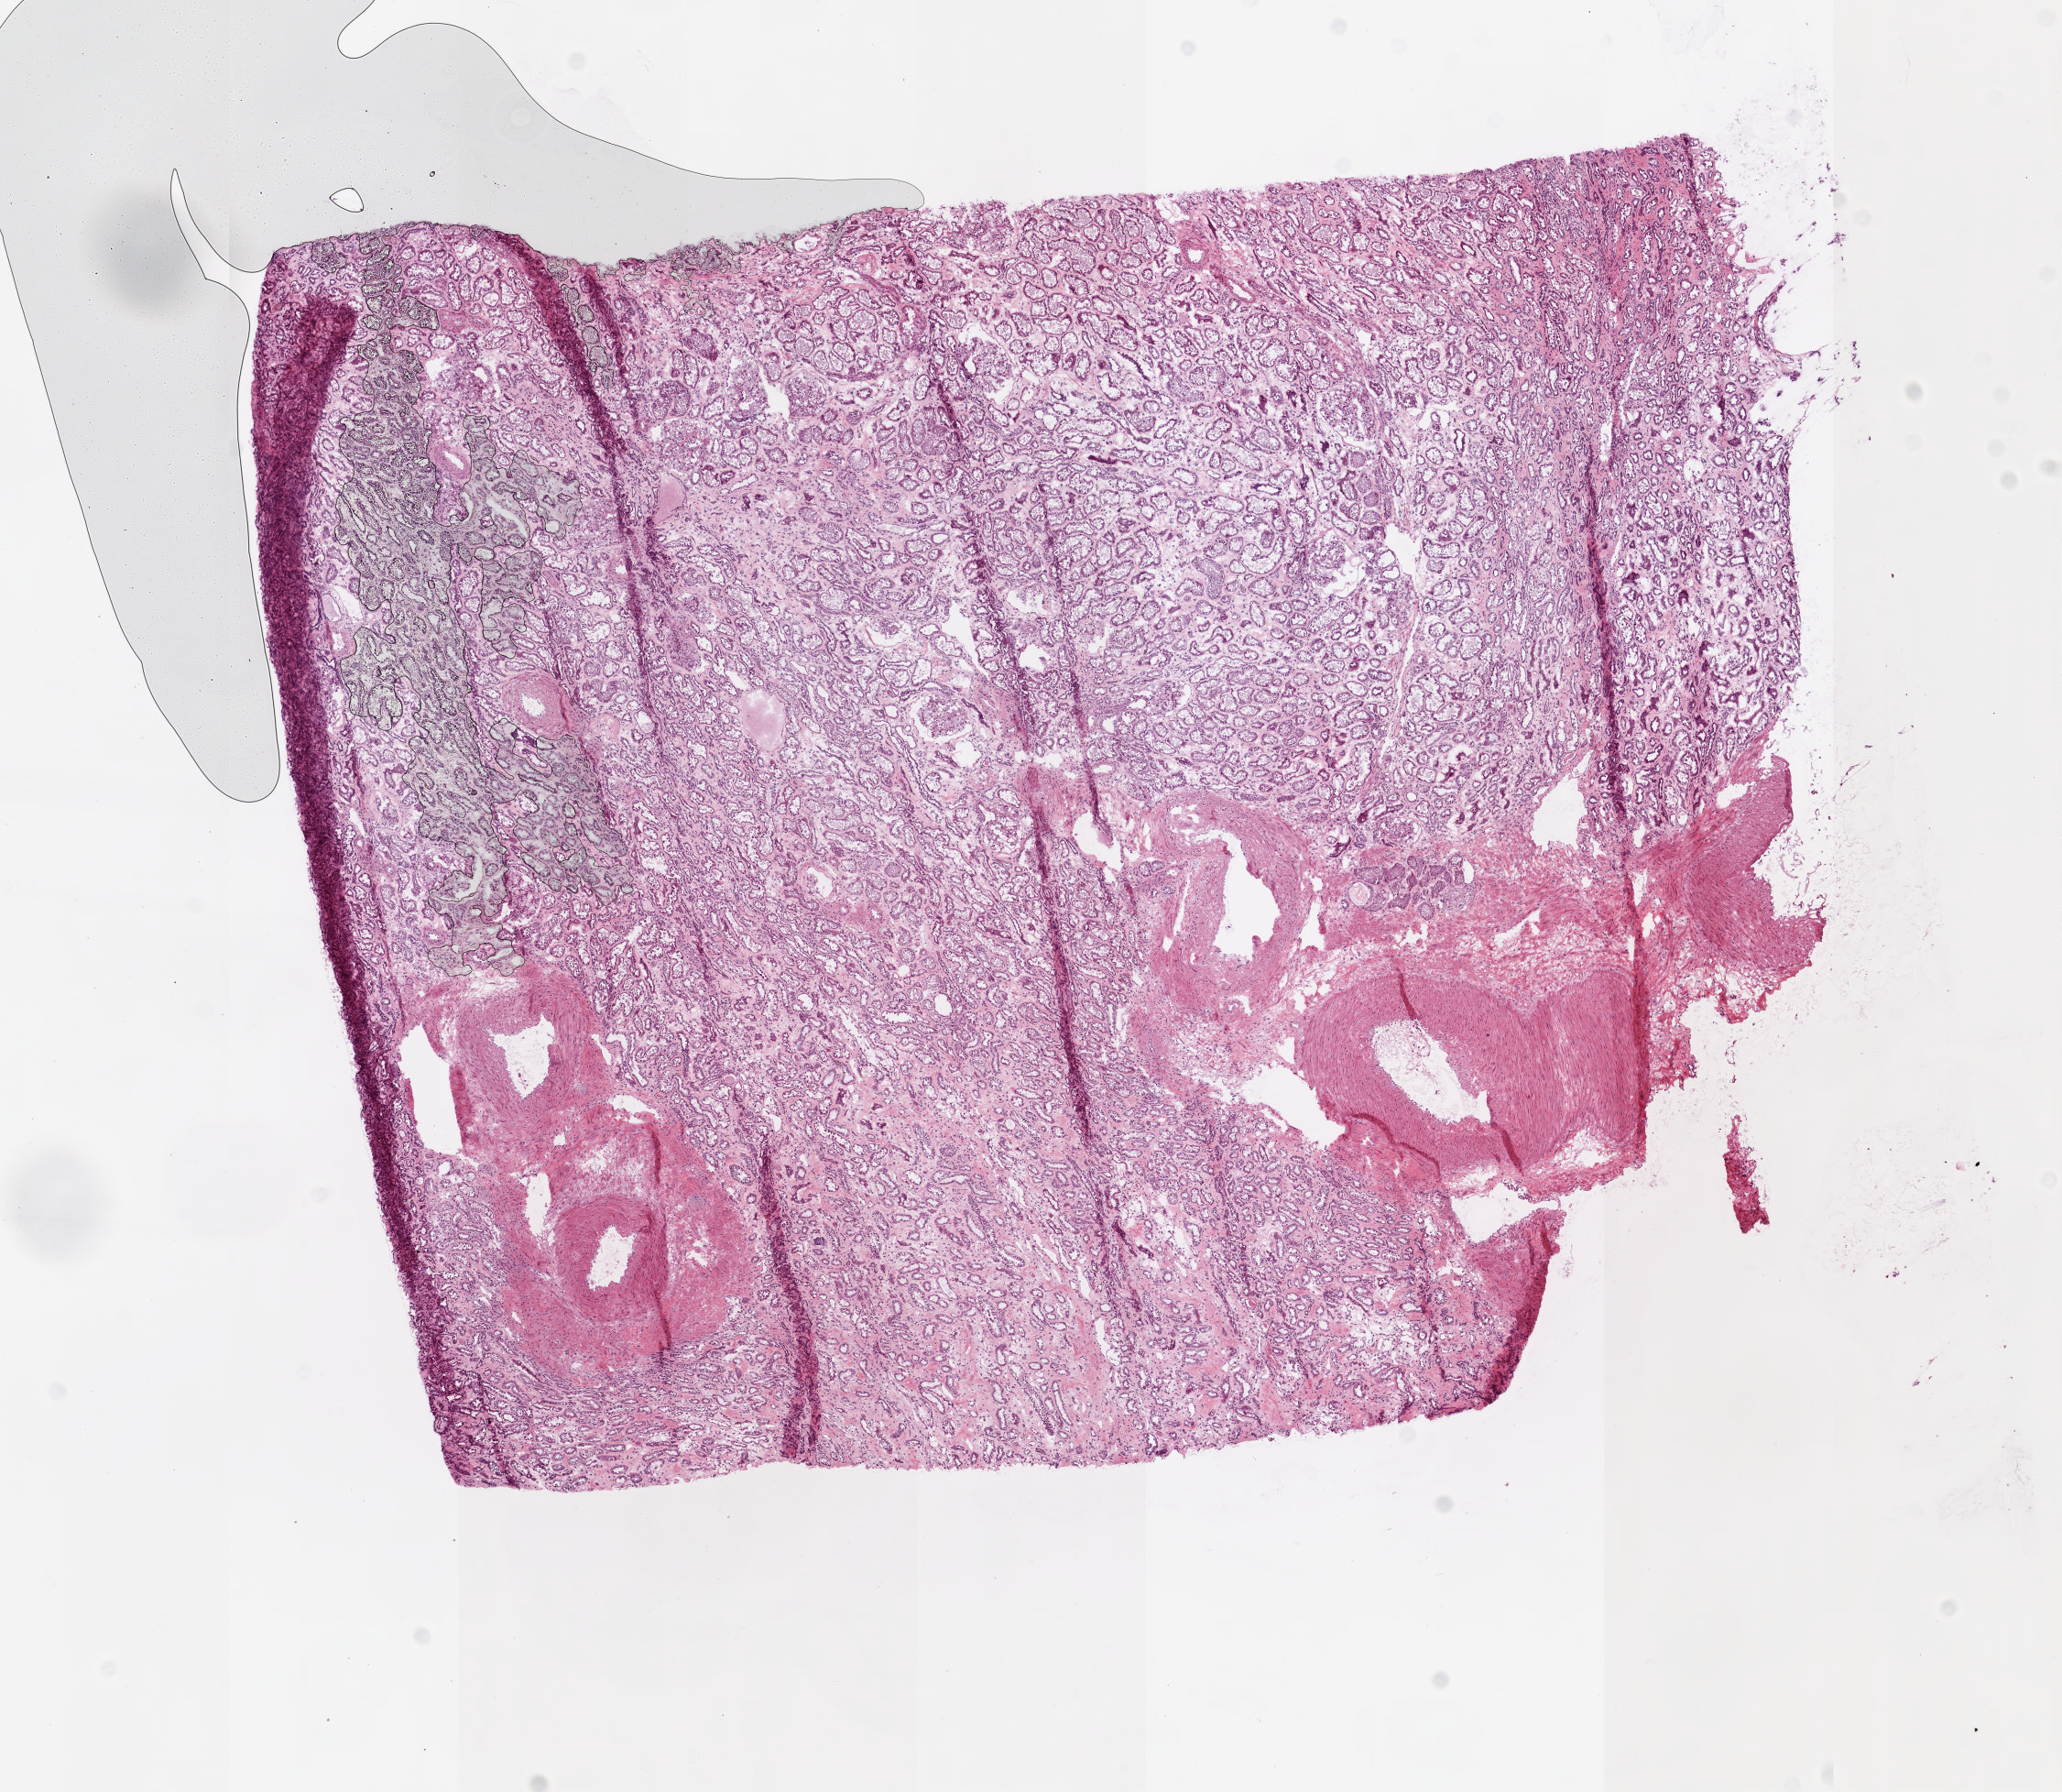
Digitized Hematoxylin and eosin (H&E) stained tissue section (whole slide) — a low-resolution overview of the entire scanned area, about 8.9 x 7.8 mm (from a 20x scan), frozen section from the top of the tissue portion, solid tissue normal (non-tumour tissue) sample from the kidney. Male, age 79 years at initial diagnosis.
* this section: solid tissue normal (non-tumour) sample from the same patient
* patient diagnosis: Clear cell adenocarcinoma, NOS